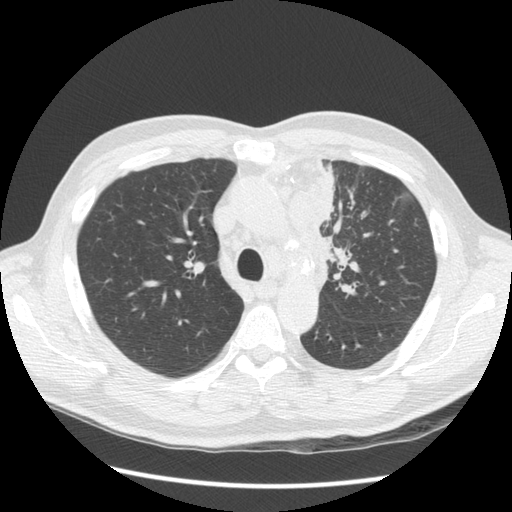
Low-dose screening chest CT, one axial slice. Slice 98 of 136 in the series (ordered by position). Lung window (W 1500 / L -600 HU). 2.5 mm slice thickness. 512 × 512 image matrix, field of view 360 × 360 mm.
Structures marked on this image (expert manual segmentation):
- lesion 1 (tumor, upper lobe of left lung): bounding box [x1, y1, x2, y2] px = [291, 171, 333, 286]